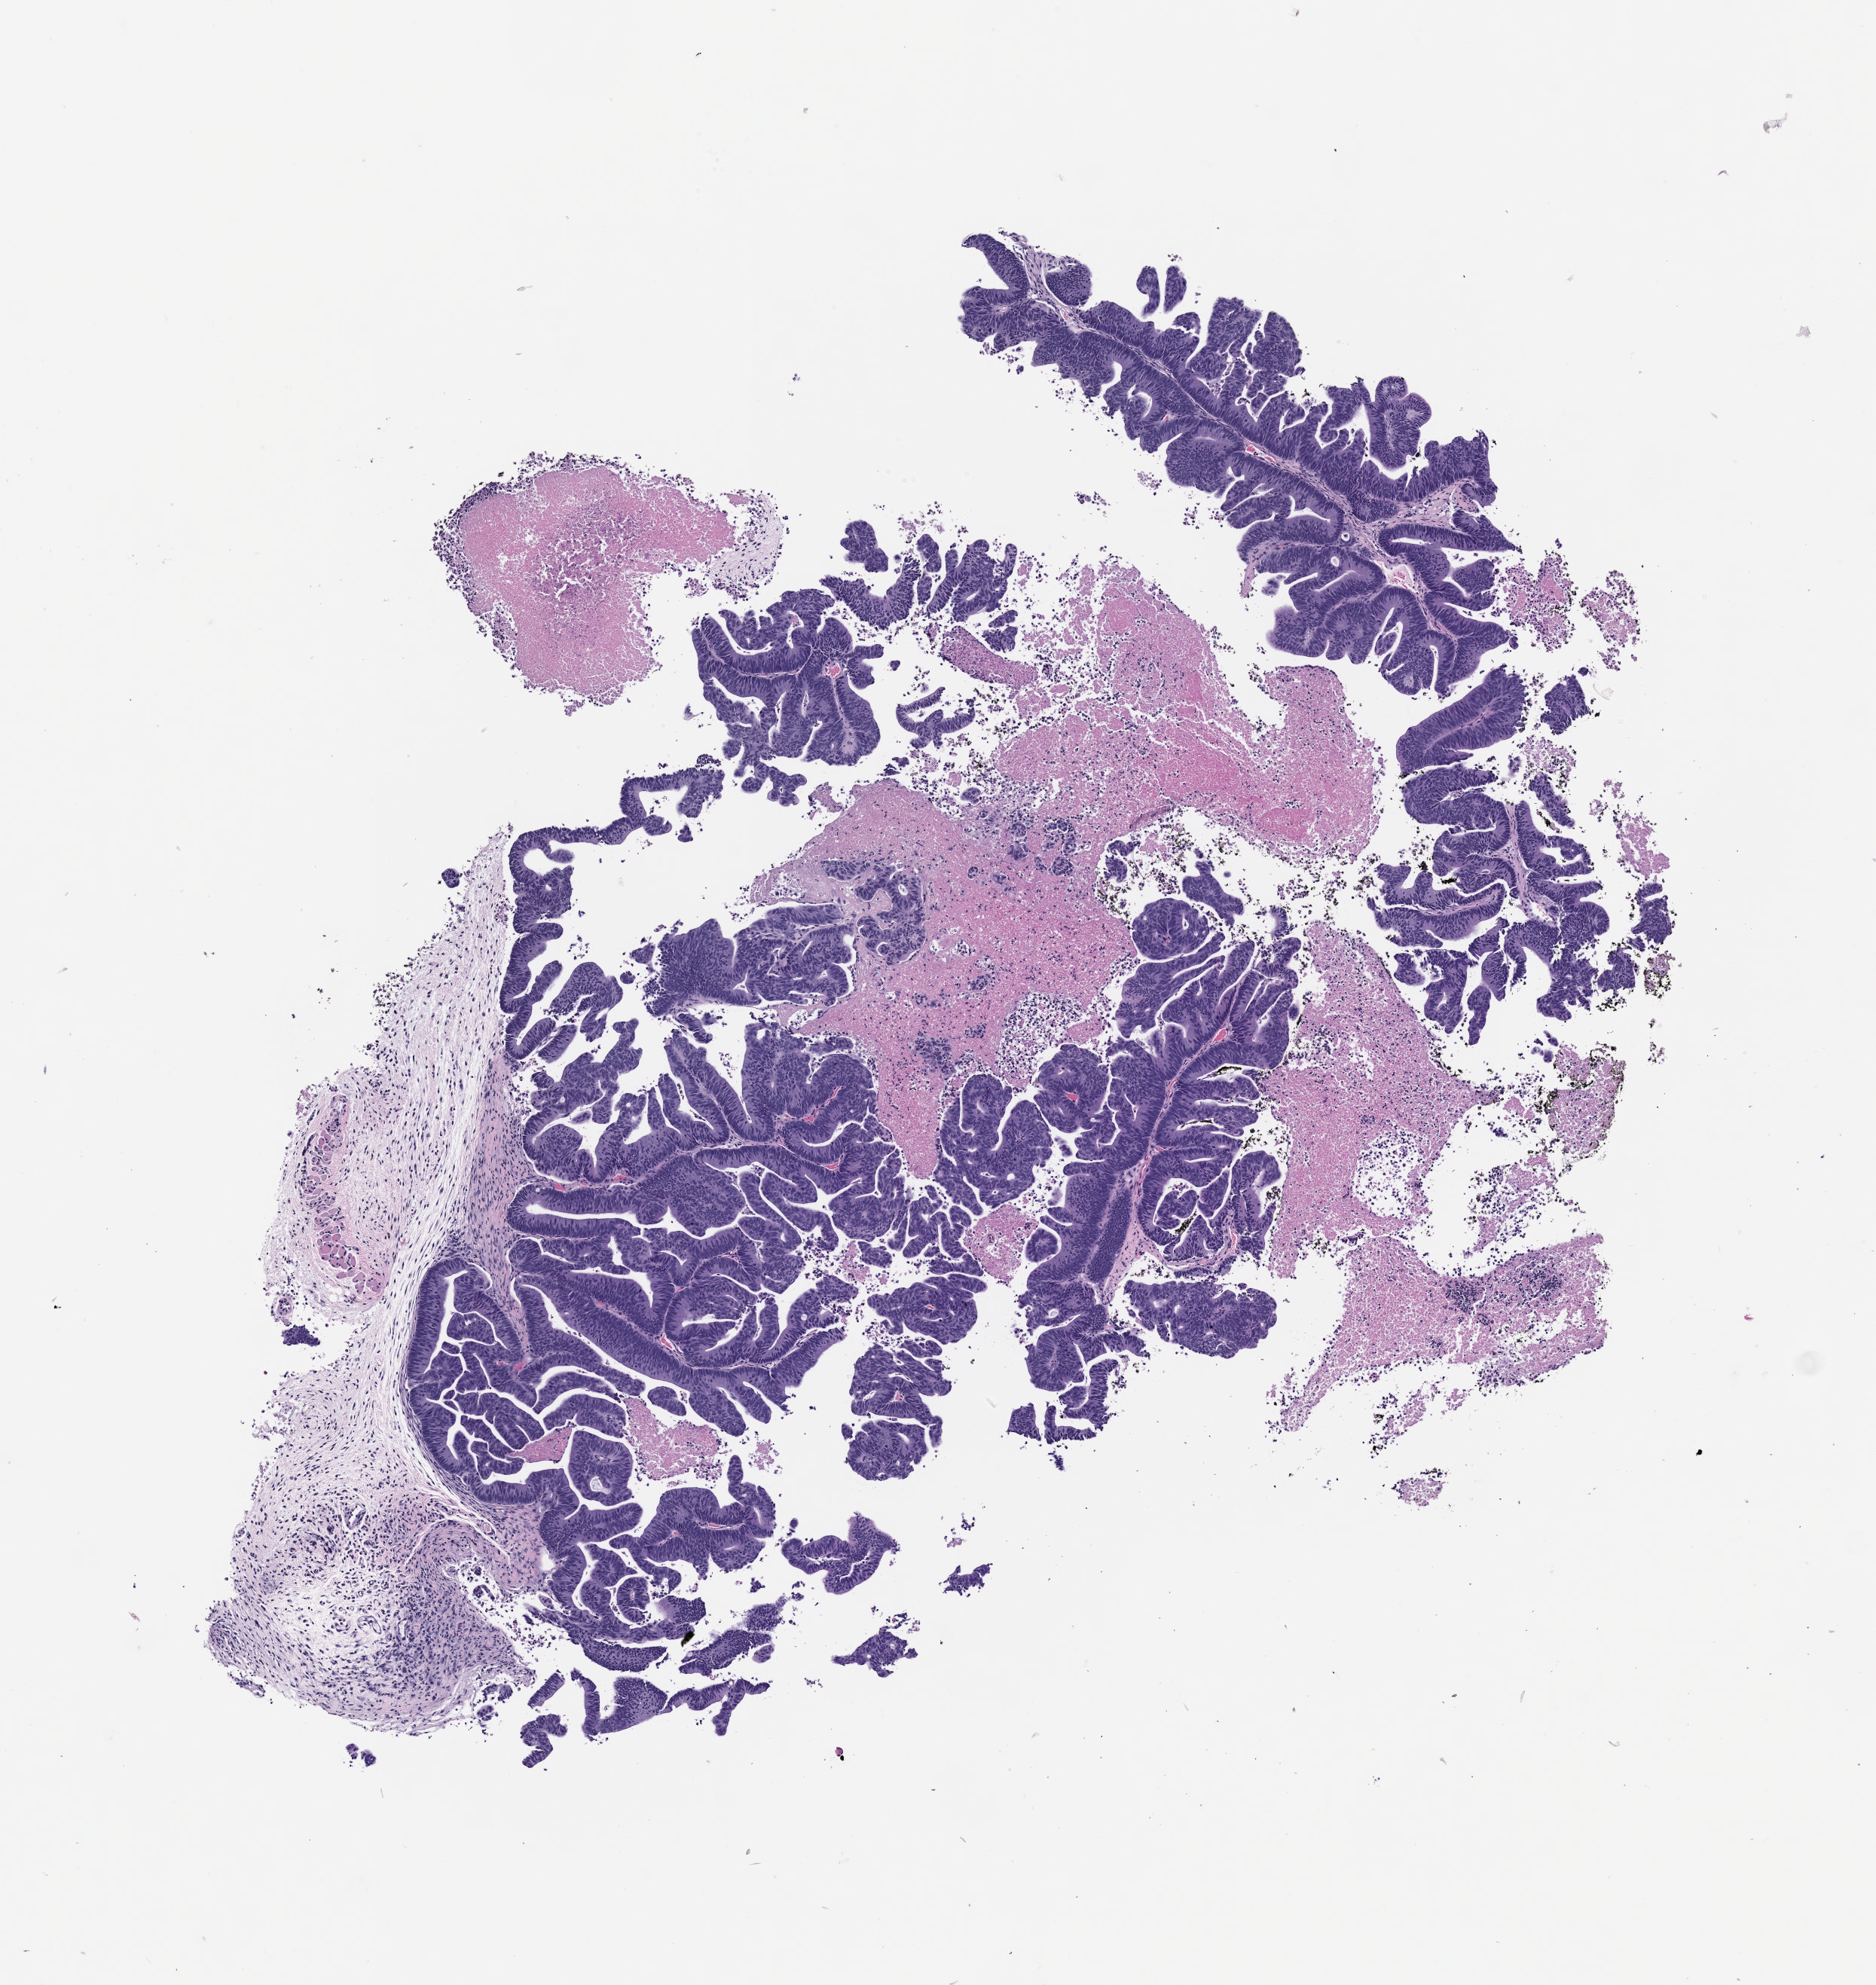
Whole-slide image, haematoxylin and eosin: patient-derived xenograft (human tumor grown in a mouse), passage 3, low-resolution overview of the scanned area, about 5.0 x 5.3 mm. Formalin-fixed paraffin-embedded section. Originating tumor site category: gastrointestinal tract.
Originating patient diagnosis: Colorectal Carcinoma.